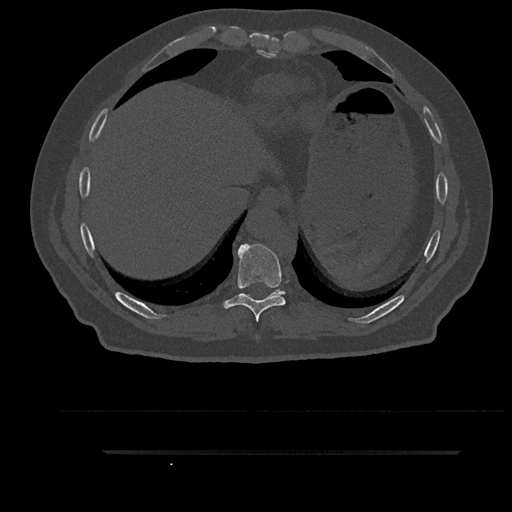
CT including the spine, one axial slice; position 420 of 797 along the scan axis; bone window (W 1800 / L 400 HU); 0.5 mm slice thickness; 512 × 512 image matrix. Male patient, age 63 years. Case-level facts recorded for this patient, not image findings: primary cancer: renal; vertebrae with lytic lesions (as recorded): T8.
Structures marked on this image (semi-automatically segmented with operator editing):
- T10 vertebra: bounding box <271,289,284,296> (left, top, right, bottom; pixels)
- T9 vertebra: <218,244,292,322>